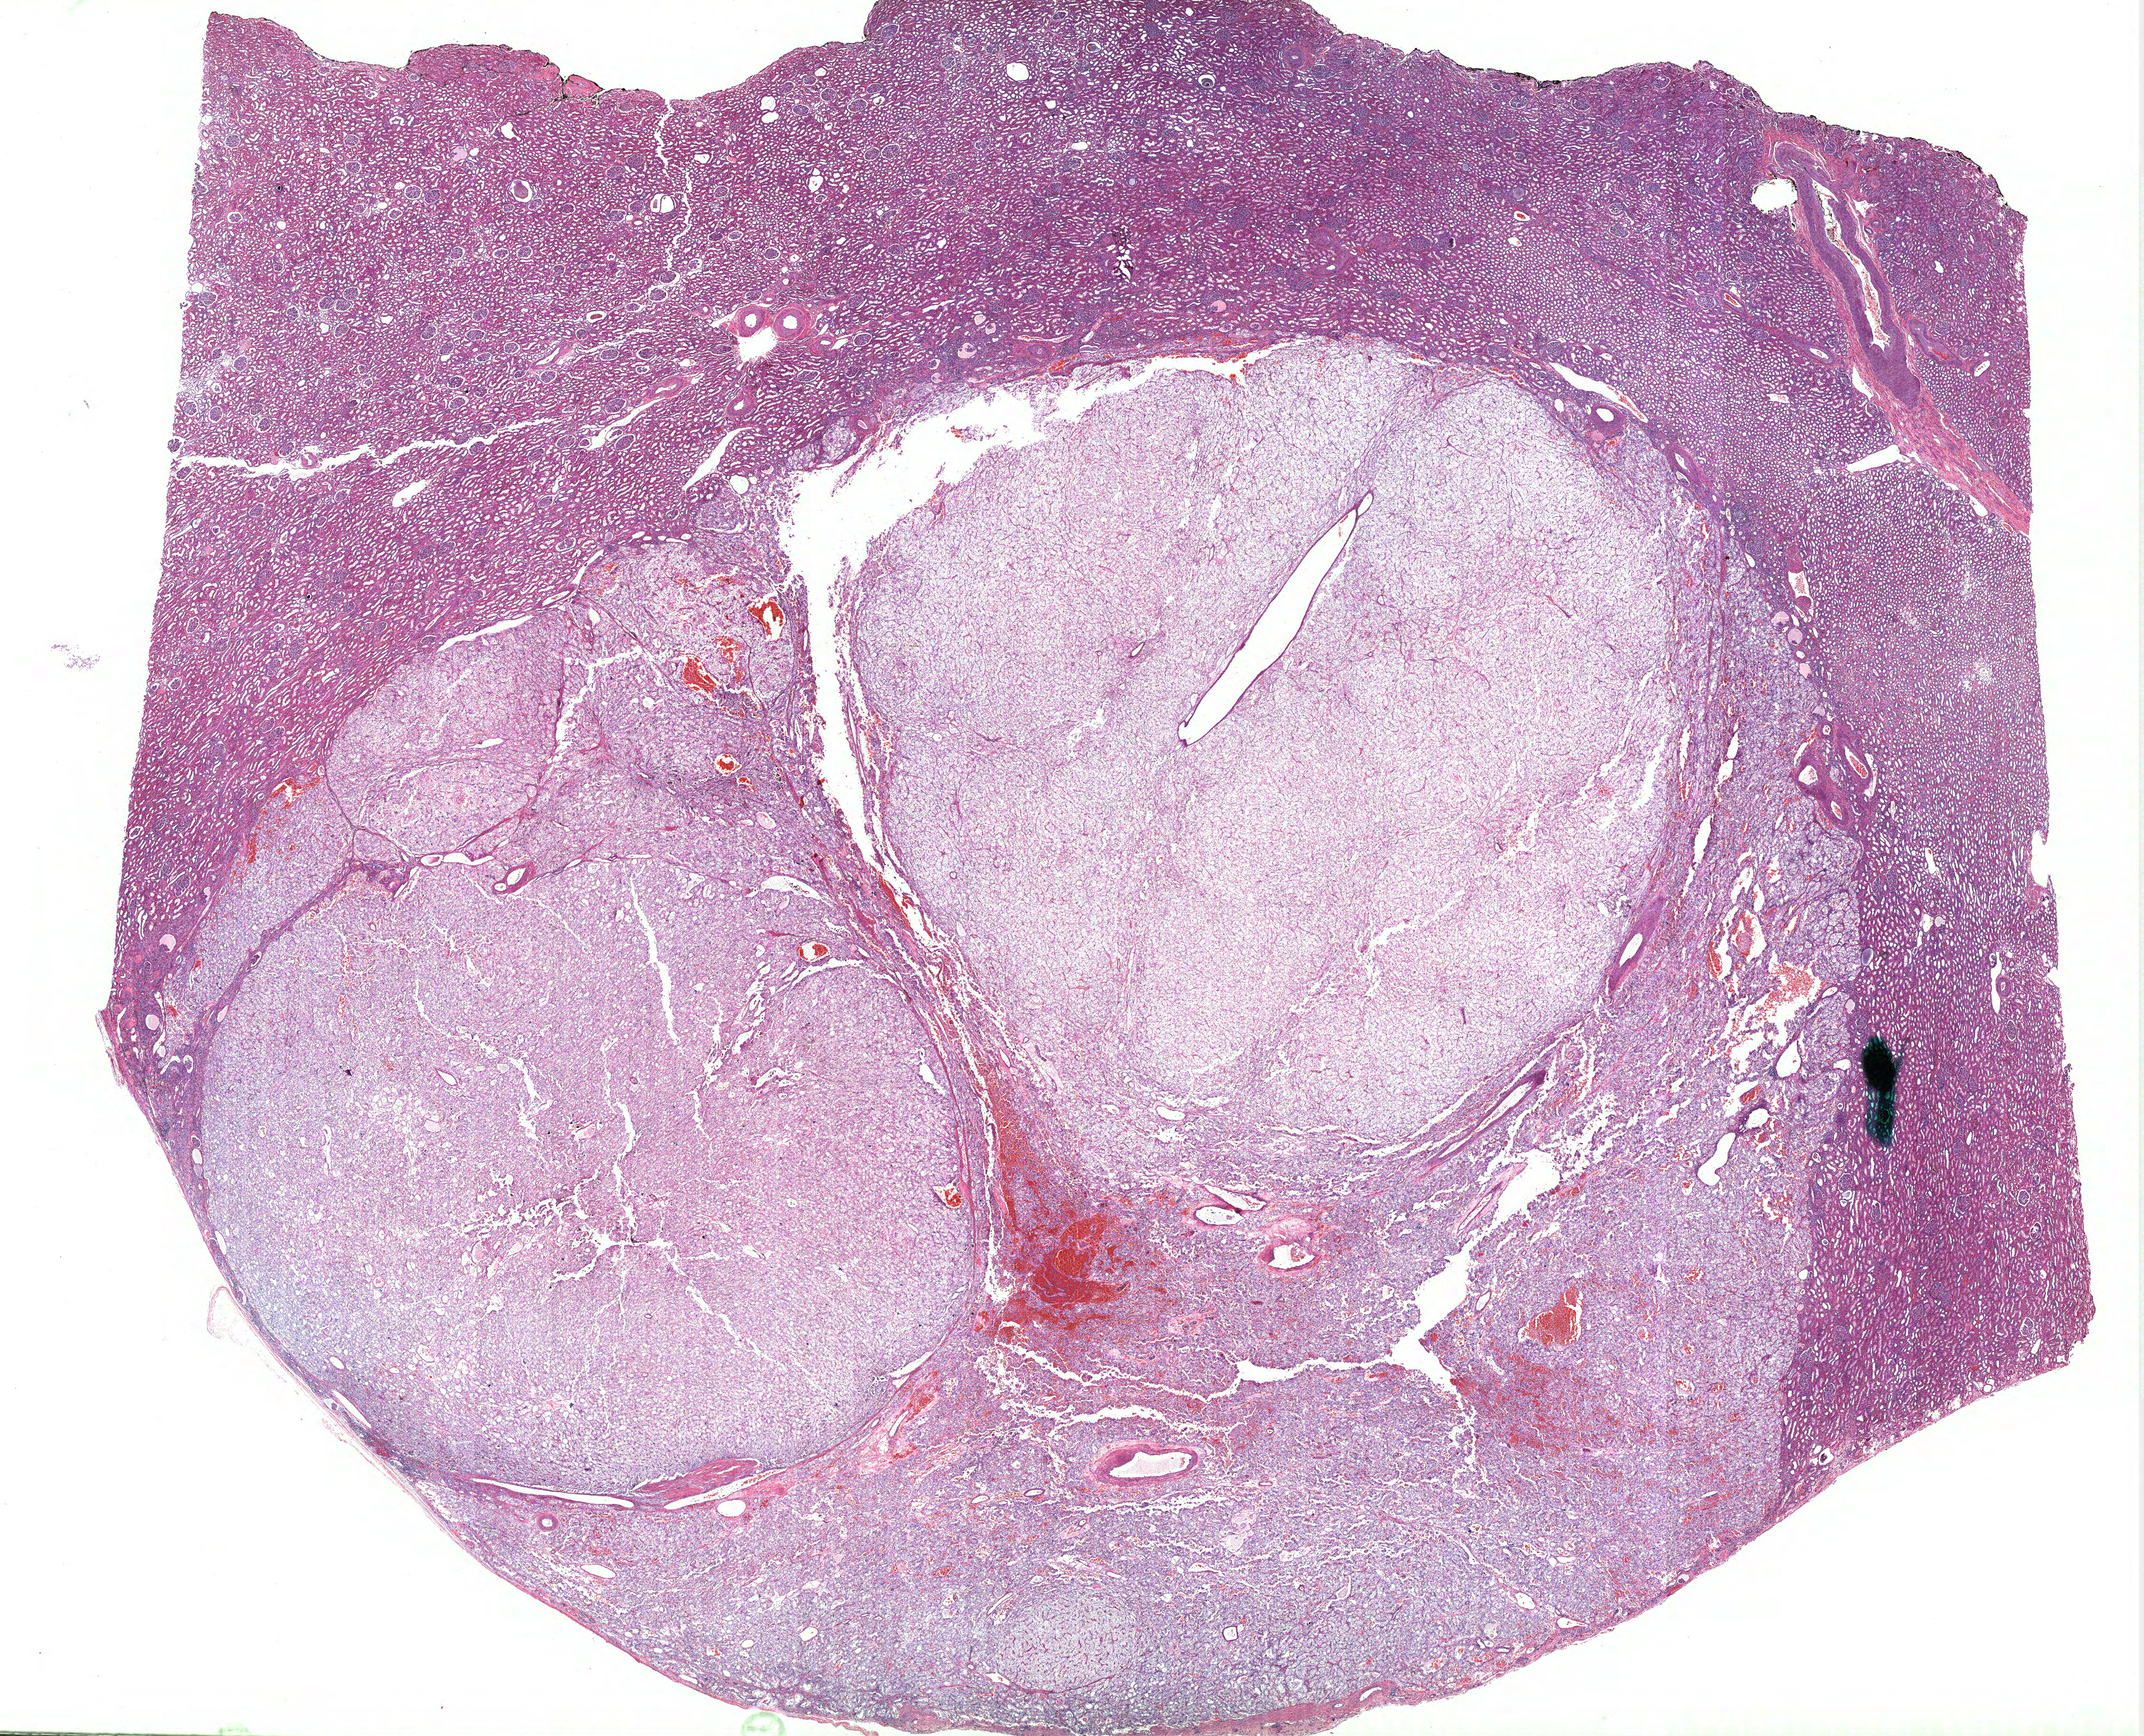
Digitized H&E tissue section (whole slide), low-resolution overview of the scanned area, about 27.1 x 21.9 mm (slide scanned at 40x). FFPE section. Primary tumour sample from the kidney. Male patient; age at initial diagnosis 54 years. Histologic grade: G3 (poorly differentiated).
• diagnosis: Clear cell adenocarcinoma, NOS
• AJCC pathologic stage: I